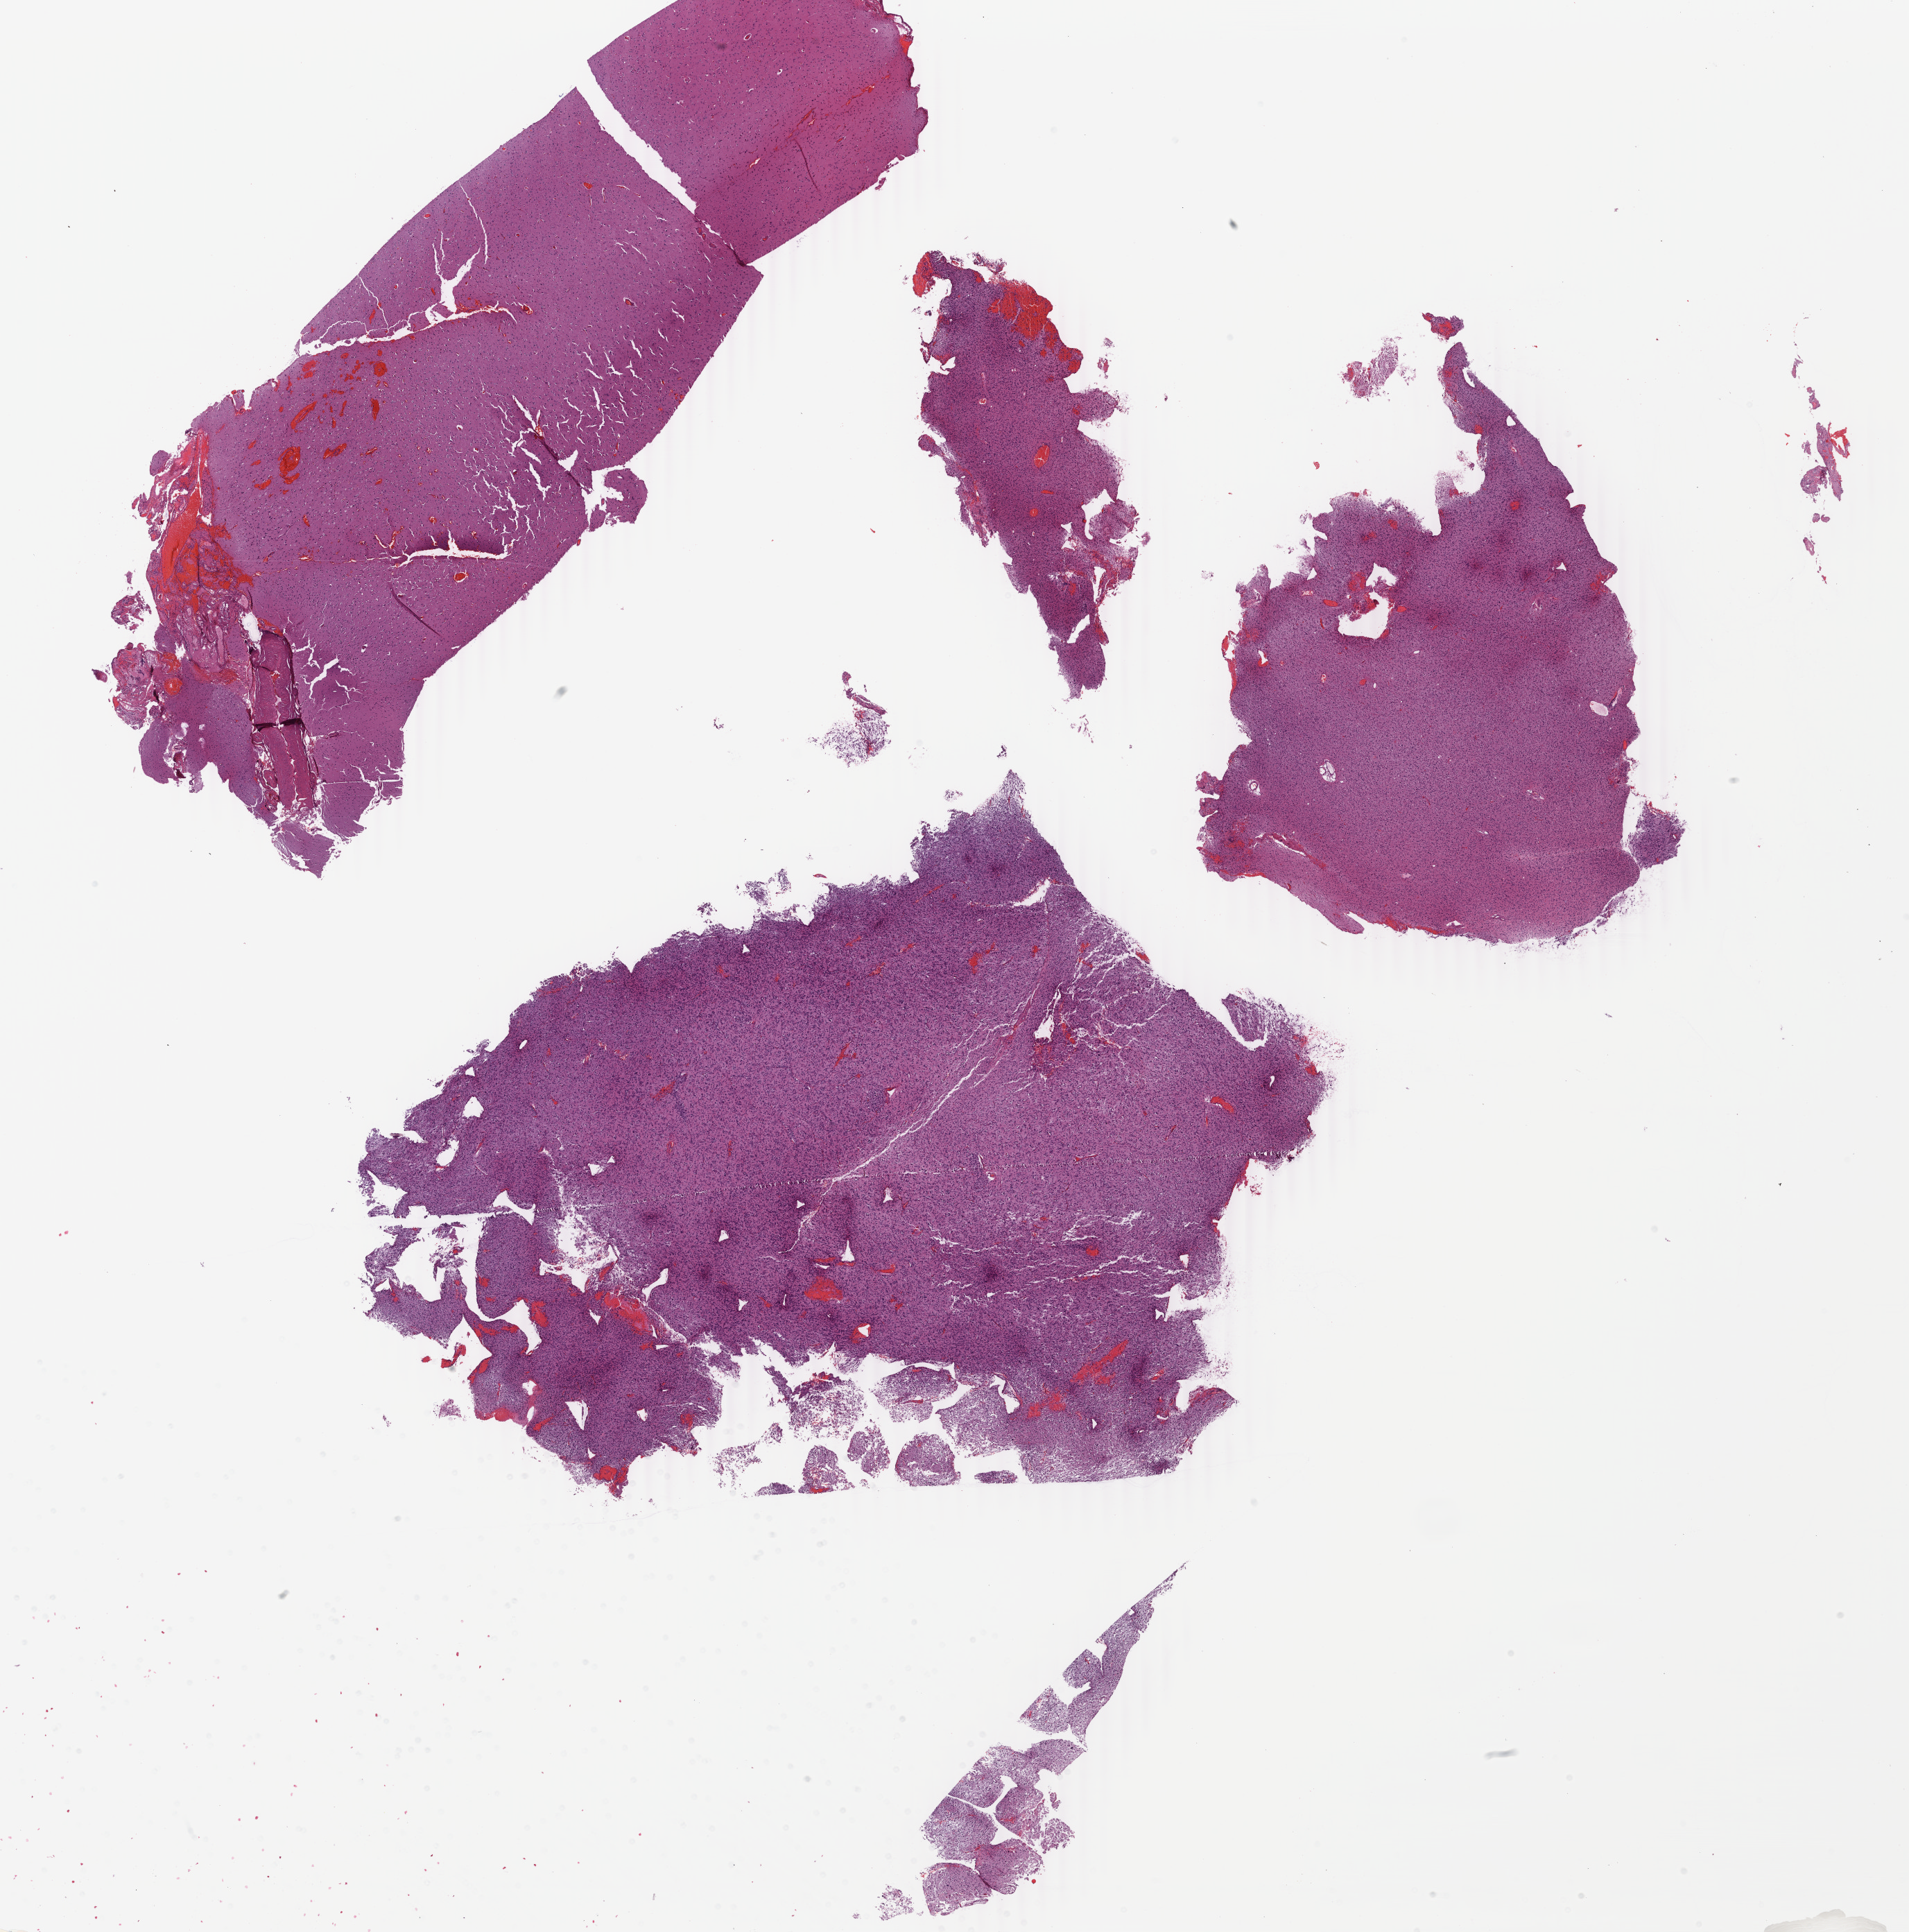
Whole-slide histology image, H&E-stained, whole scanned area (about 21.9 x 22.2 mm) shown as a low-resolution overview. Formalin-fixed paraffin-embedded (FFPE) diagnostic section. Brain, primary tumour sample. Patient: male, age at initial diagnosis 22 years. Histologic grade: G3 (poorly differentiated).
• histologic diagnosis: Astrocytoma, anaplastic (cerebrum)
• laterality: left